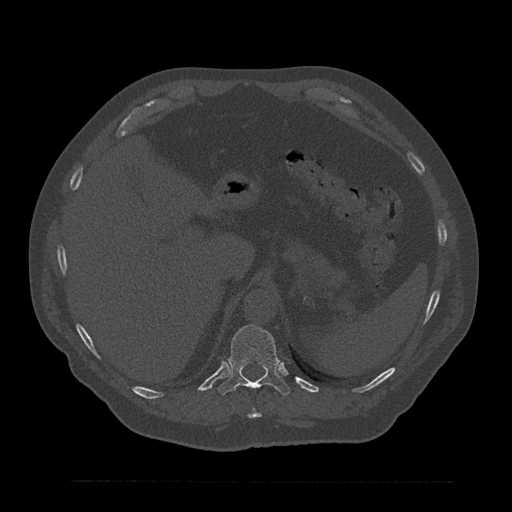
CT including the spine, one axial slice; position 302 of 797 along the scan axis; reconstruction kernel Br40s/3; bone window (W 1800 / L 400 HU); 512 × 512 image matrix, field of view 430 × 430 mm. Patient: male, 61 years. From the clinical record (not read from this slice): primary cancer: prostate.
Structures marked on this image (semi-automatically segmented with operator editing):
- T10 vertebra: bounding box <248,408,262,419> (left, top, right, bottom; pixels)
- T11 vertebra: <218,325,290,396>